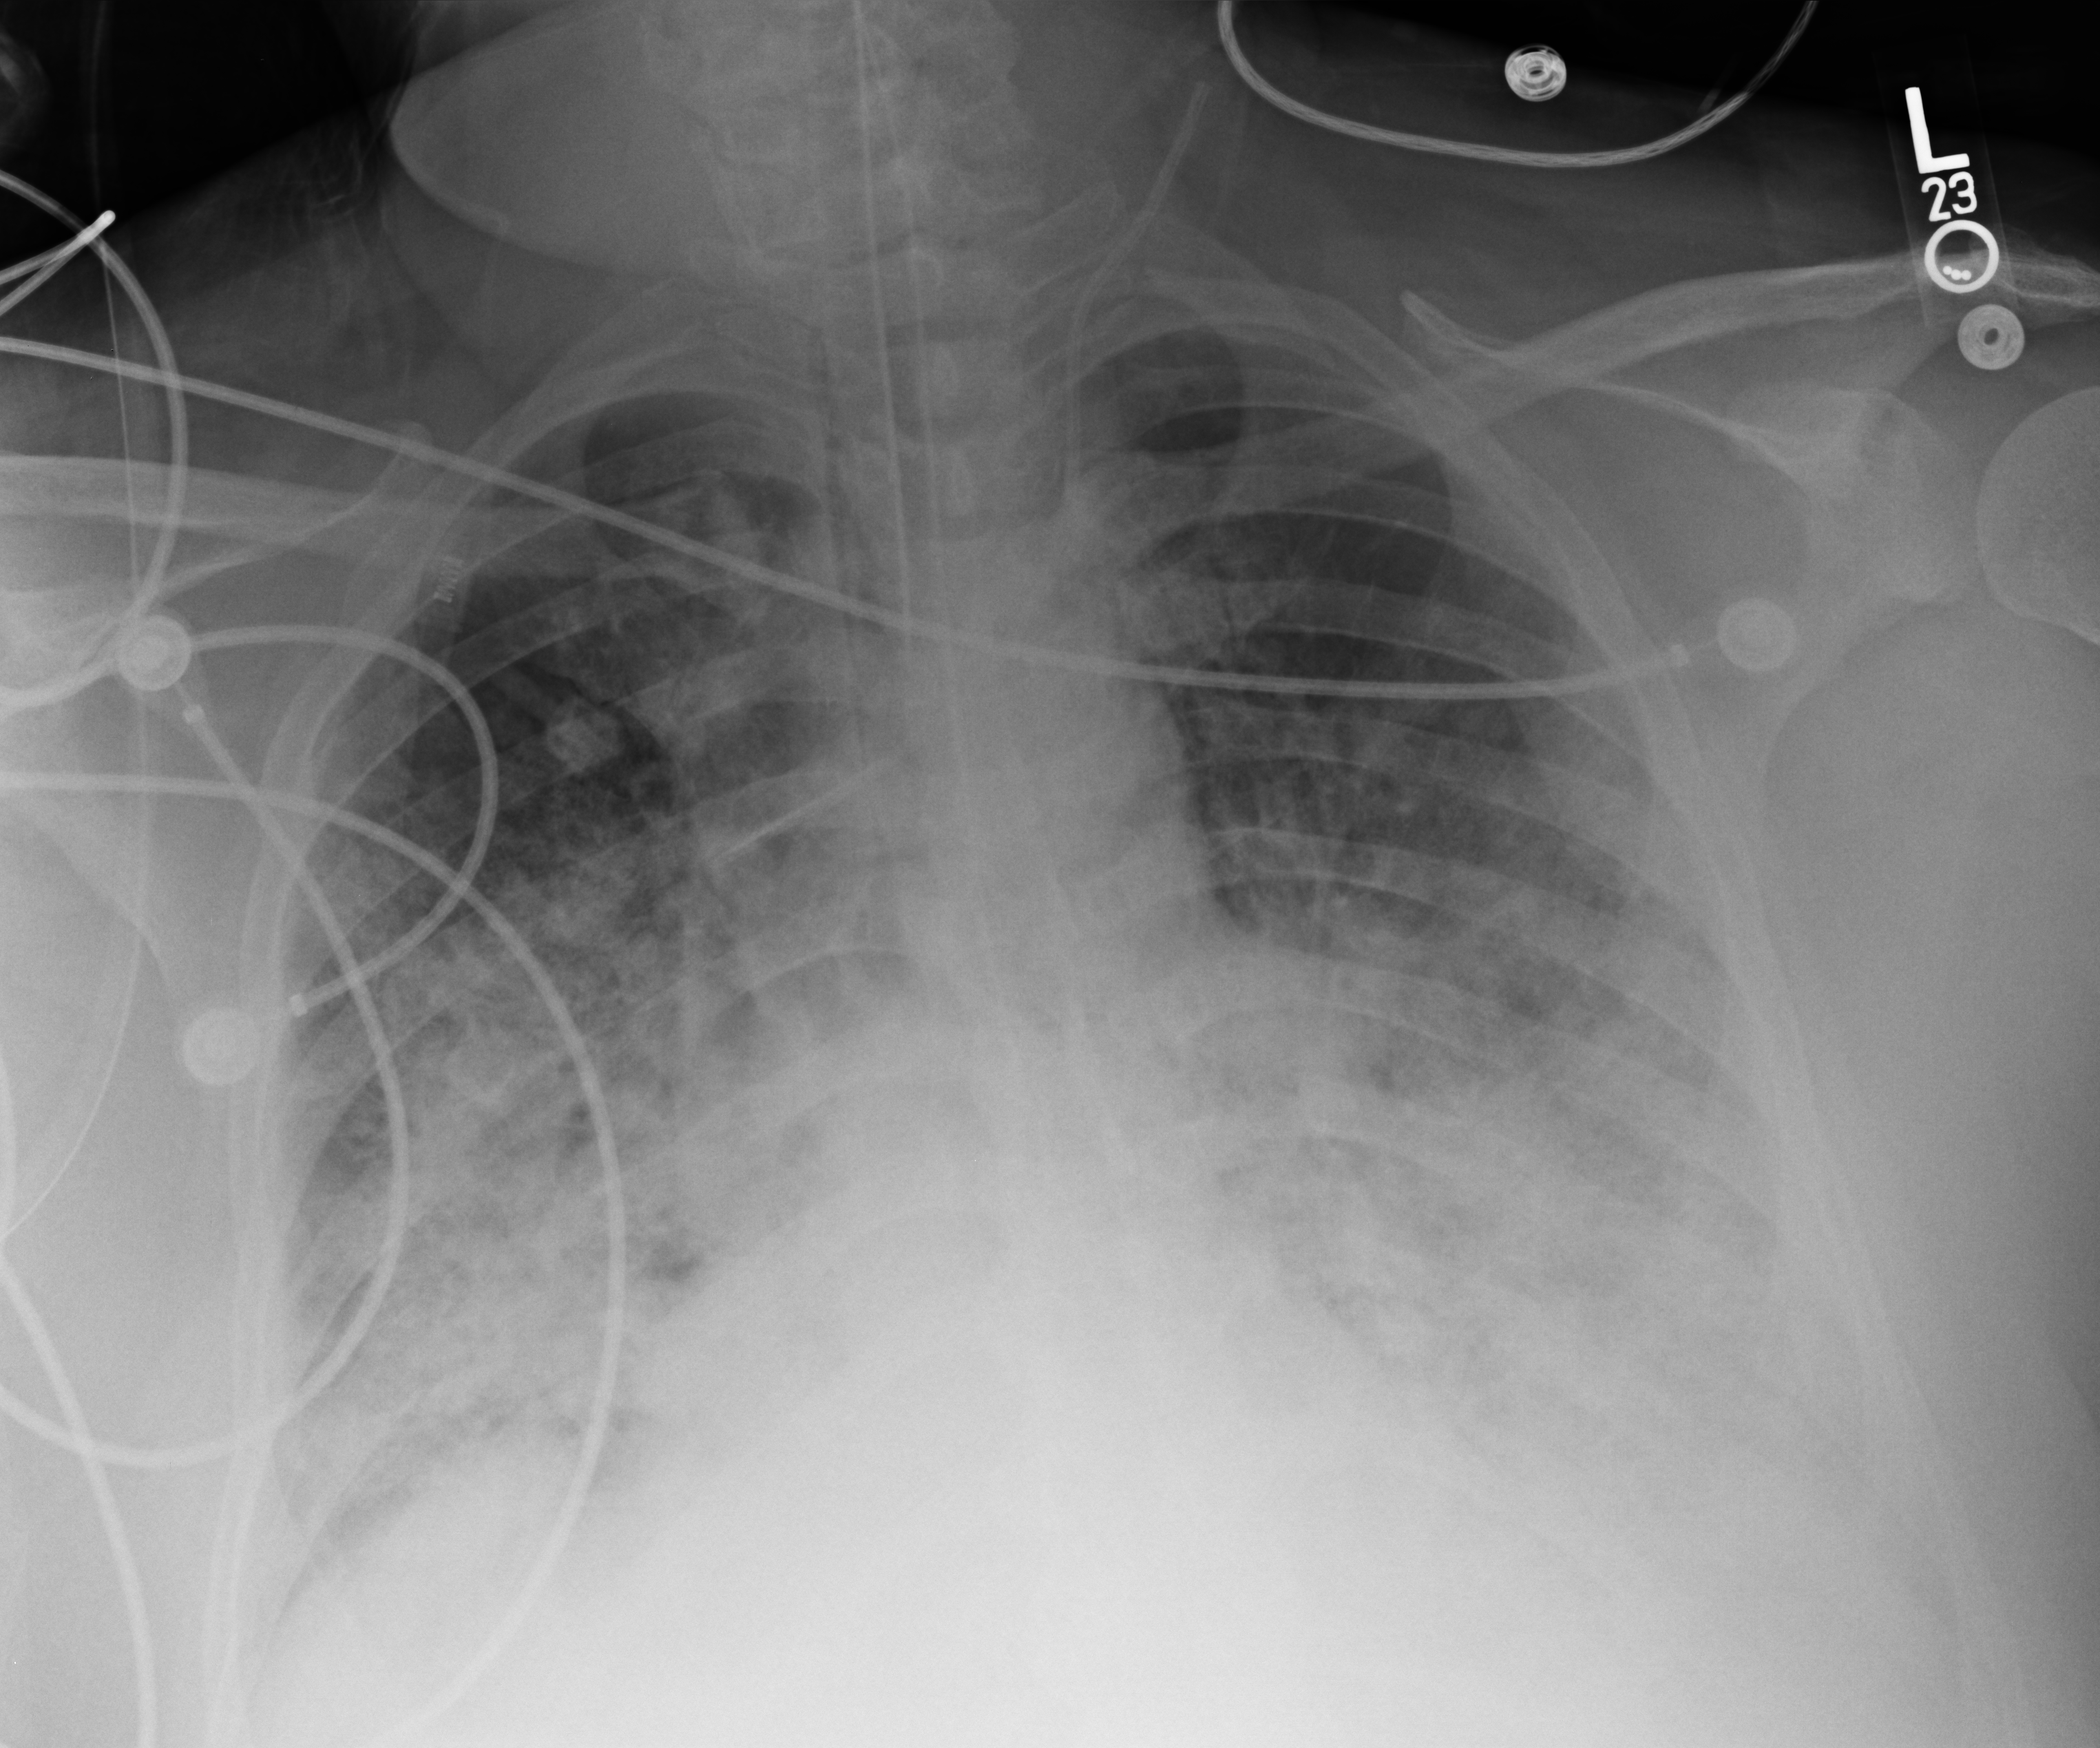
Chest X-ray (portable), anteroposterior (AP) projection. Patient hospitalised with COVID-19, aged 18–59 years.
From the hospital-stay record, not from the radiograph (when in the stay this image was taken is not recorded): mechanically ventilated during this hospital stay: yes.